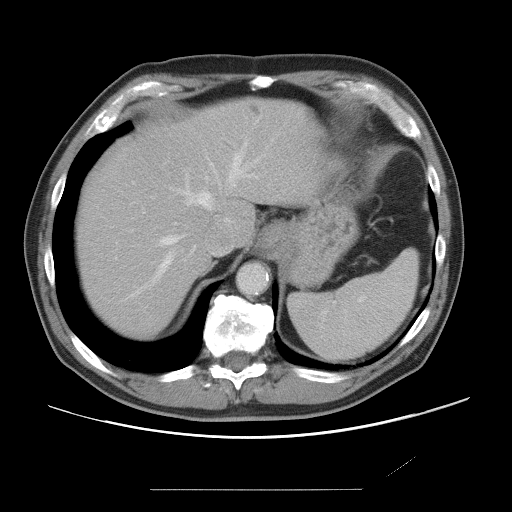
Contrast-enhanced abdominal CT, one axial slice; position 59 of 87 along the scan axis; 120 kVp; intravenous contrast given; soft-tissue window (W 400 / L 40 HU); 512 × 512 image matrix, field of view 406 × 406 mm. Male patient, age 74 years. Case-level facts recorded for this patient, not image findings: diagnosis: colorectal cancer liver metastases, imaged before liver resection; multiple liver metastases: yes; largest metastasis: 1.1 cm.
Annotated regions visible in this slice (expert manual segmentation):
- hepatic veins: bounding box <130,144,257,297> (left, top, right, bottom; pixels)
- liver: <77,99,314,340>
- planned liver remnant (the part of the liver to remain after resection): <77,99,313,340>
- portal vein (with intrahepatic branches): <115,177,208,259>
- liver metastasis: <251,105,261,115>